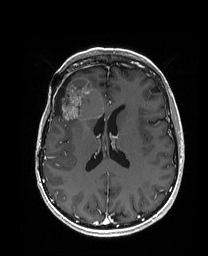
Brain MRI from a brain-tumour surgery series, one axial slice. Position 80 of 192 along the scan axis. T1-weighted post-contrast. 1 mm slice thickness. 208 × 256 image matrix. From the clinical record (not read from this slice): histopathology: Metastatic Carcinoma from Breast primary; tumour location: Right Frontal.
Annotated regions visible in this slice (manually delineated by an expert):
- previous resection cavity: bounding box [x1, y1, x2, y2] px = [54, 77, 71, 116]
- tumour: [55, 77, 104, 120]